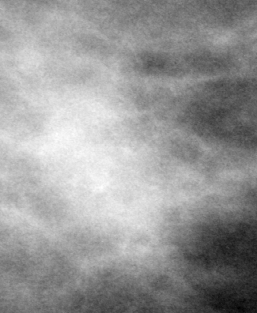
Cropped region of a digitized screen-film mammogram centred on a radiologist-marked abnormality; left breast; CC view.
- Calcifications, morphology pleomorphic, distribution clustered; BI-RADS assessment category 4; subtlety rating 3 on a 1 (subtle) to 5 (obvious) scale; pathology (as recorded): malignant.